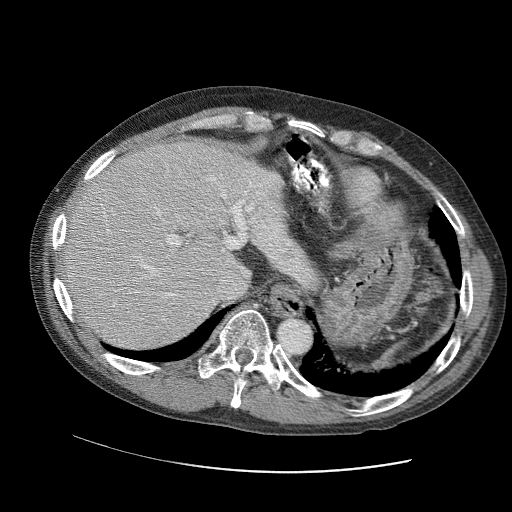
Contrast-enhanced abdominal CT (liver protocol), one axial slice; position 78 of 109 along the scan axis; reconstruction kernel STANDARD; 120 kVp; soft-tissue window (W 400 / L 40 HU); 2.5 mm slice thickness; 512 × 512 image matrix. Case-level facts recorded for this patient, not image findings: diagnosis: hepatocellular carcinoma (patient treated with transarterial chemoembolisation; whether this scan precedes or follows treatment is not stated here); TNM stage (as recorded): Stage-IIIC; Child-Pugh class: B.
Structures marked on this image (semi-automatically segmented with operator editing):
- abdominal aorta: bounding box (x1, y1, x2, y2) in pixels: (280, 318, 310, 351)
- liver parenchyma outside the tumour (the mass and vessels are separate outlines, so this box may not span the whole liver): (60, 136, 284, 348)
- liver vessels: (90, 156, 276, 322)